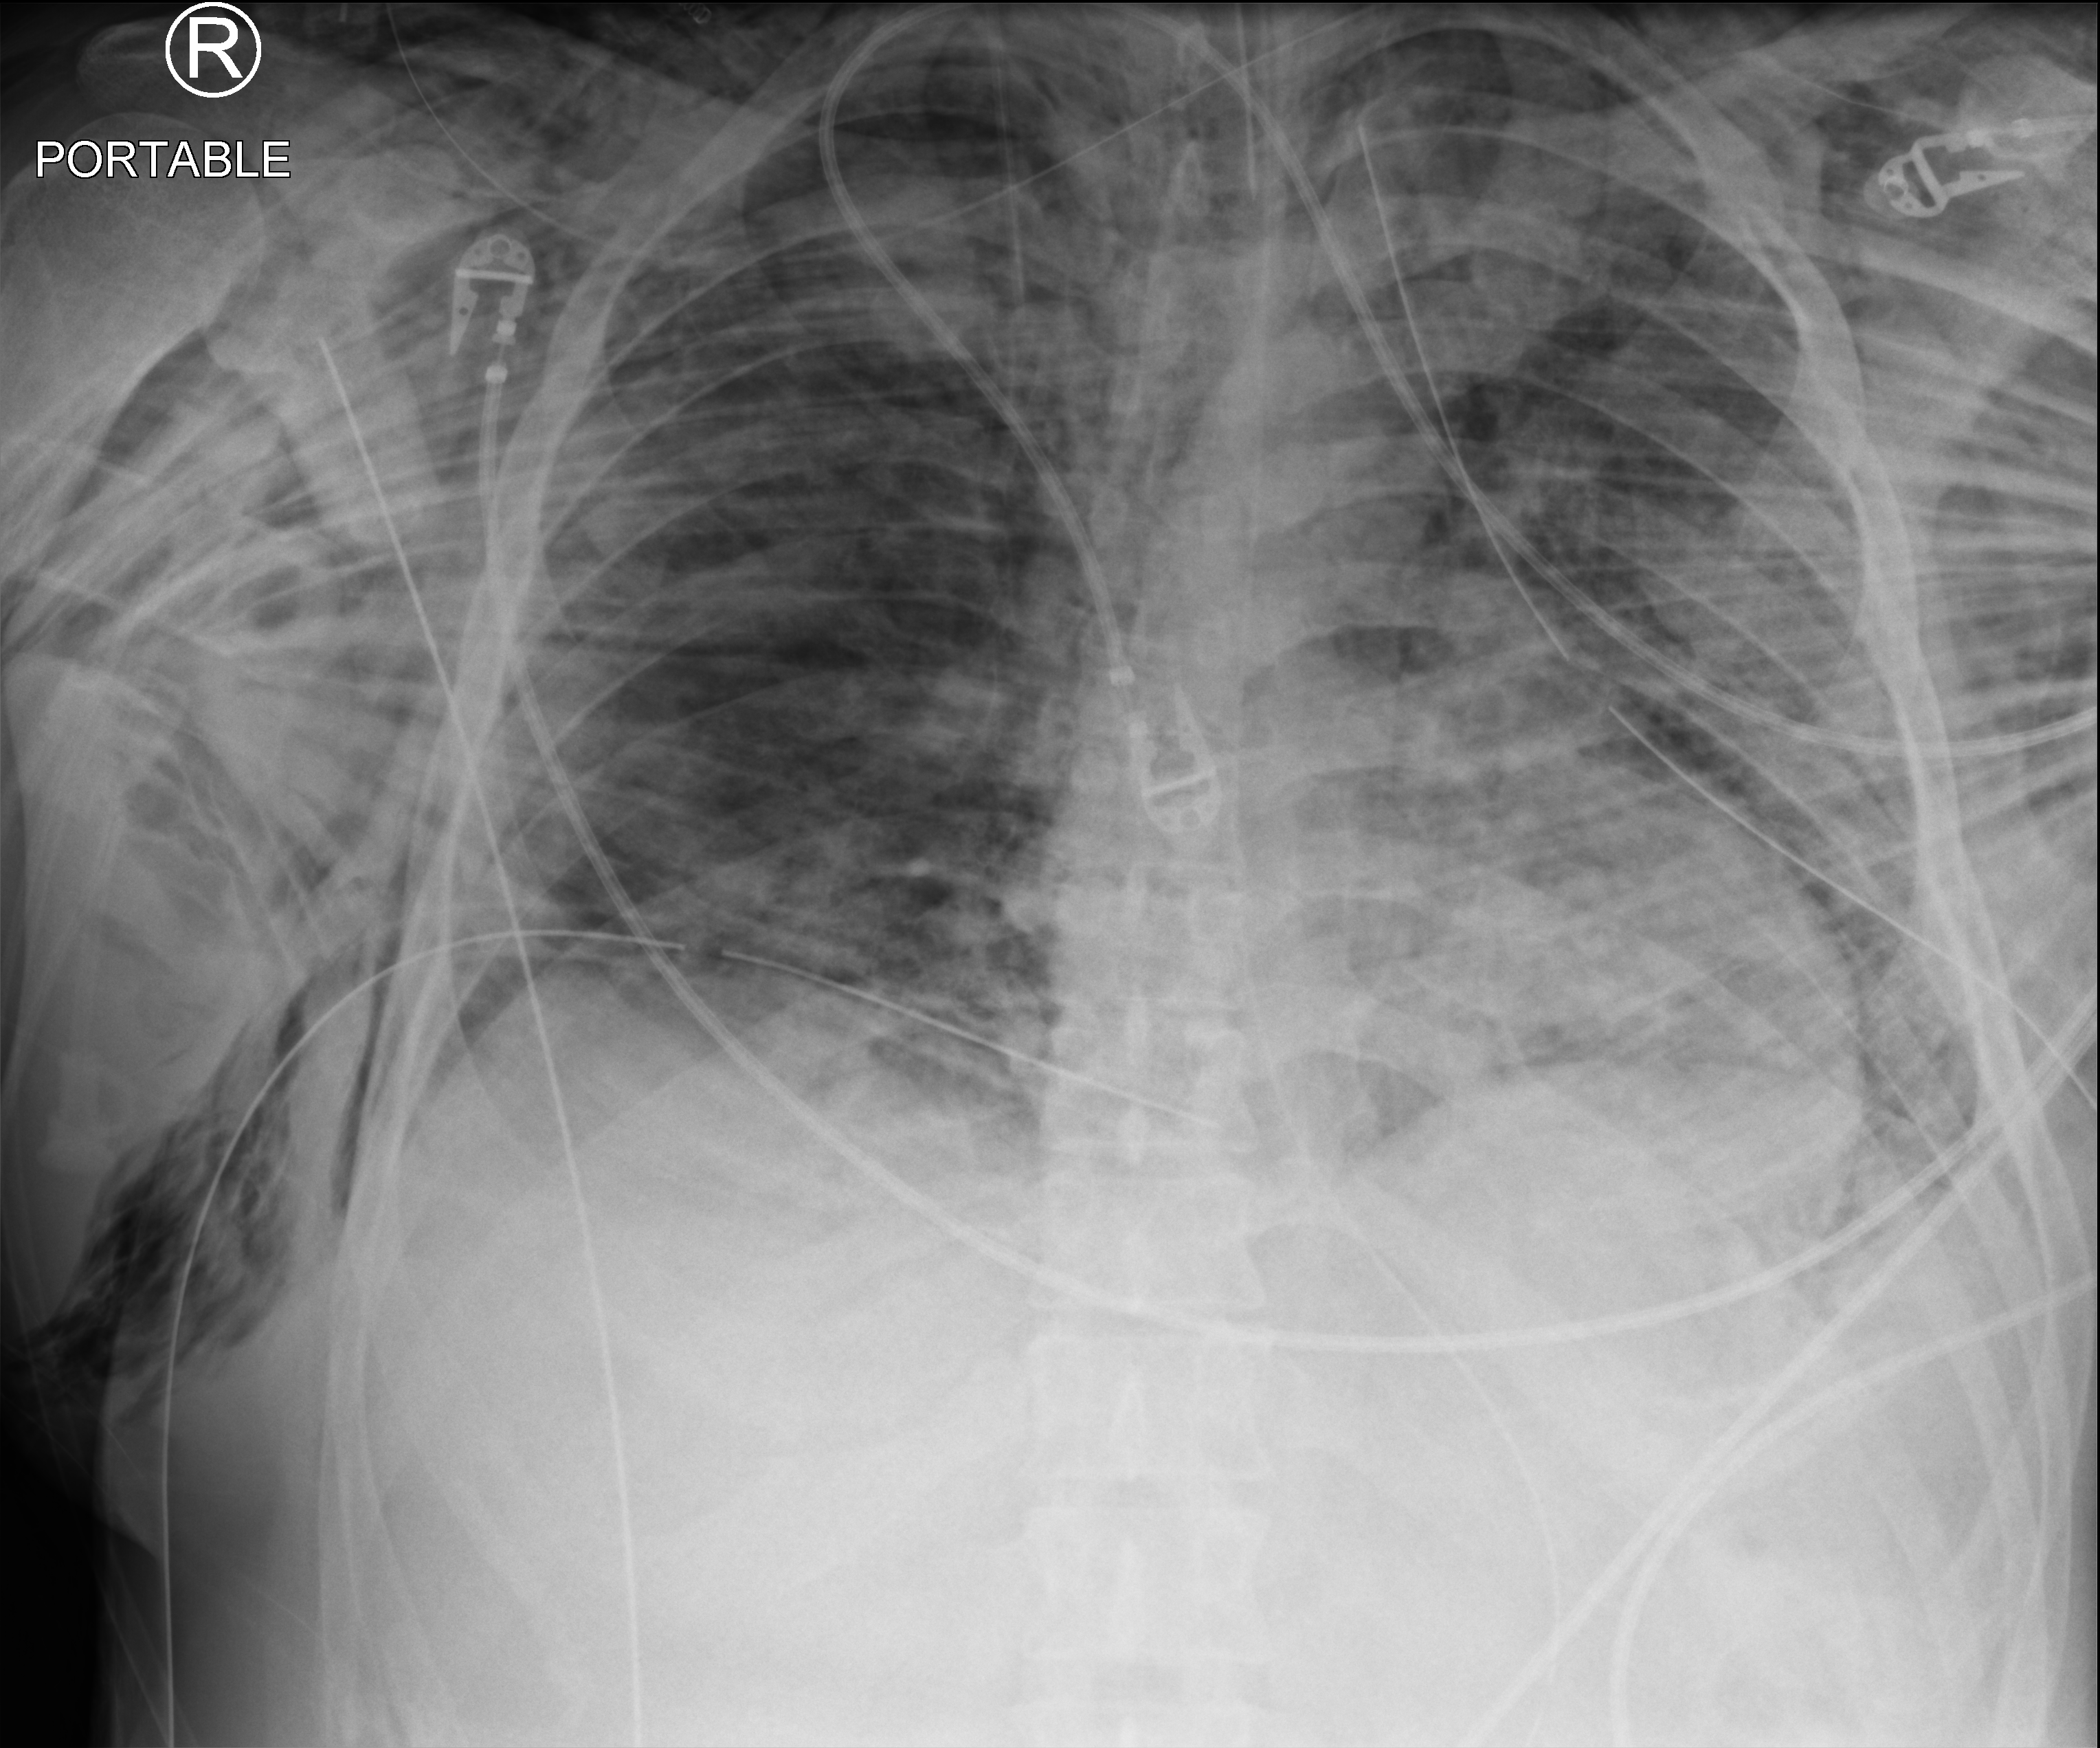
Bedside chest radiograph (computed radiography), anteroposterior (AP) projection. Male patient hospitalised with COVID-19, age 18–59 years.
From the hospital-stay record, not from the radiograph (when in the stay this image was taken is not recorded):
- admitted to intensive care during this hospital stay: yes
- length of hospital stay: 29 days